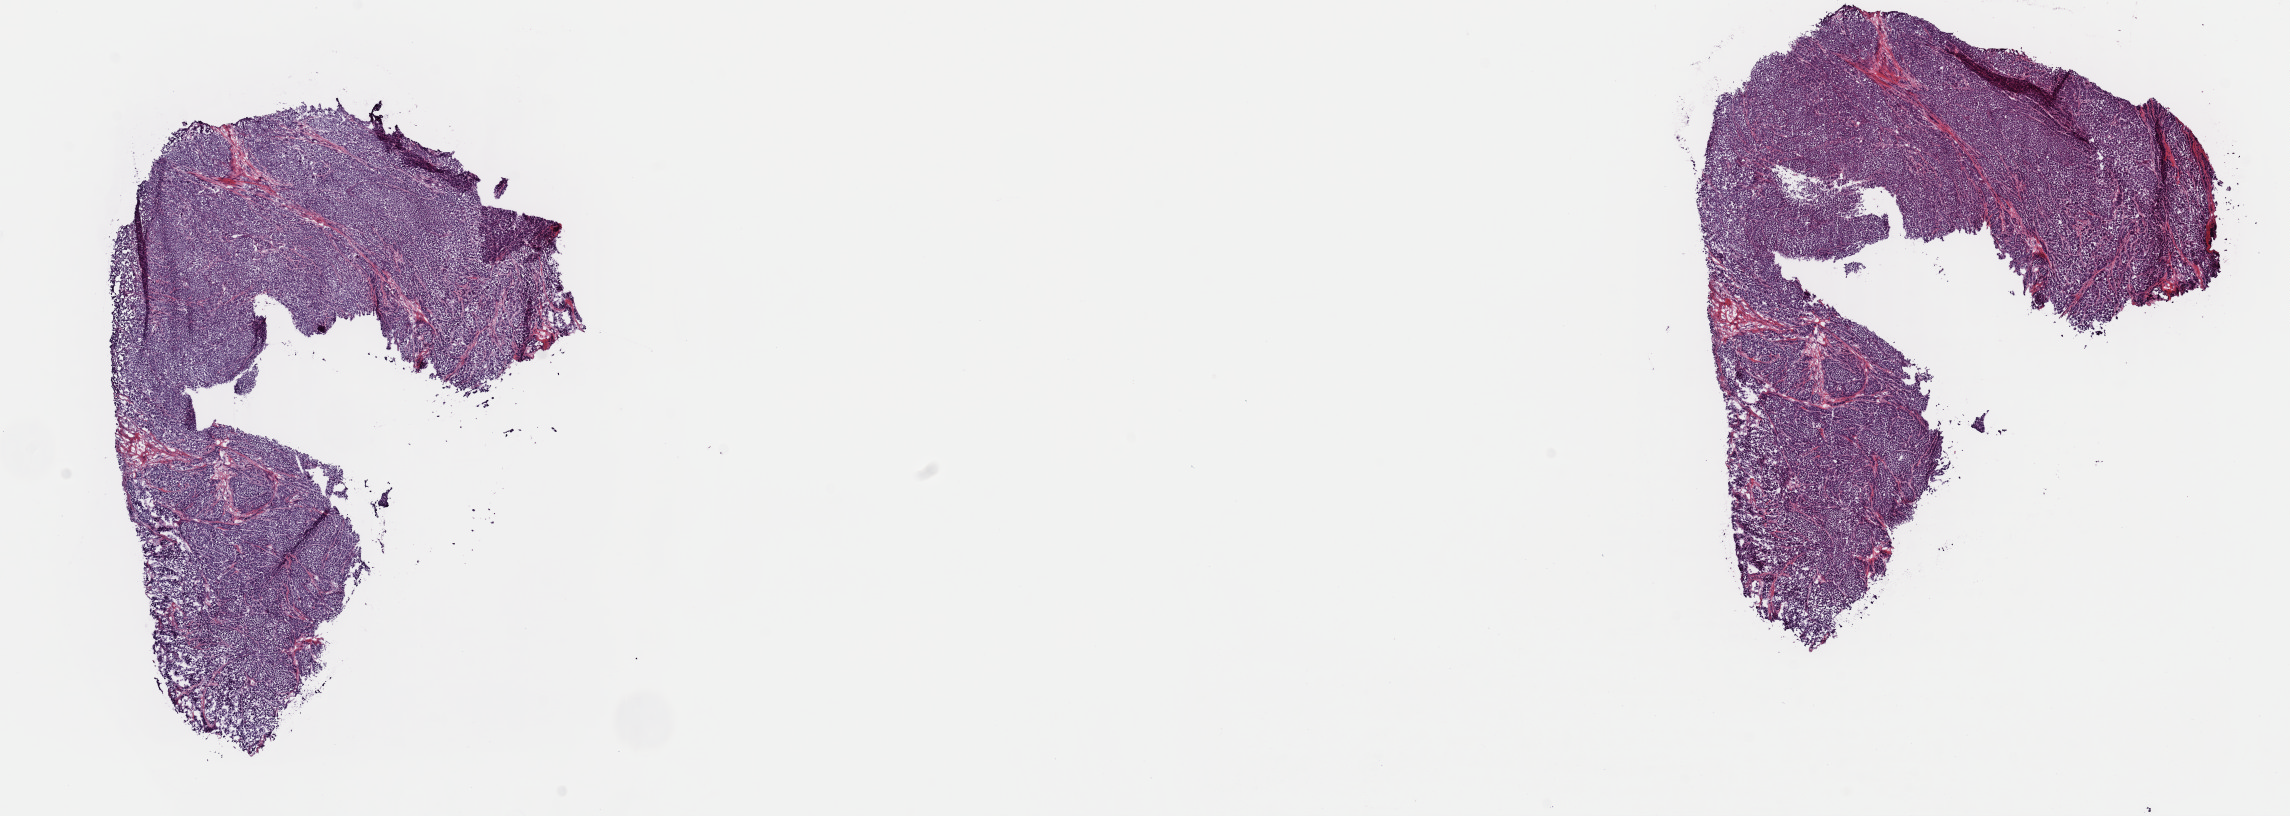
H&E-stained whole-slide image, low-resolution overview of the scanned area, about 18.1 x 6.4 mm (from a 40x scan). Frozen section from the top of the tissue portion. Primary tumour sample from the skin. Male patient; age at initial diagnosis 50 years. Pathologist review of this section (percent, as recorded): tumour cells 100%, tumour nuclei 96%, normal cells 0%, stromal cells 0%, necrosis 0%. Inflammatory infiltration, as recorded: lymphocyte infiltration 0%, monocyte infiltration 0%, neutrophil infiltration 0%.
• histologic diagnosis: Nodular melanoma